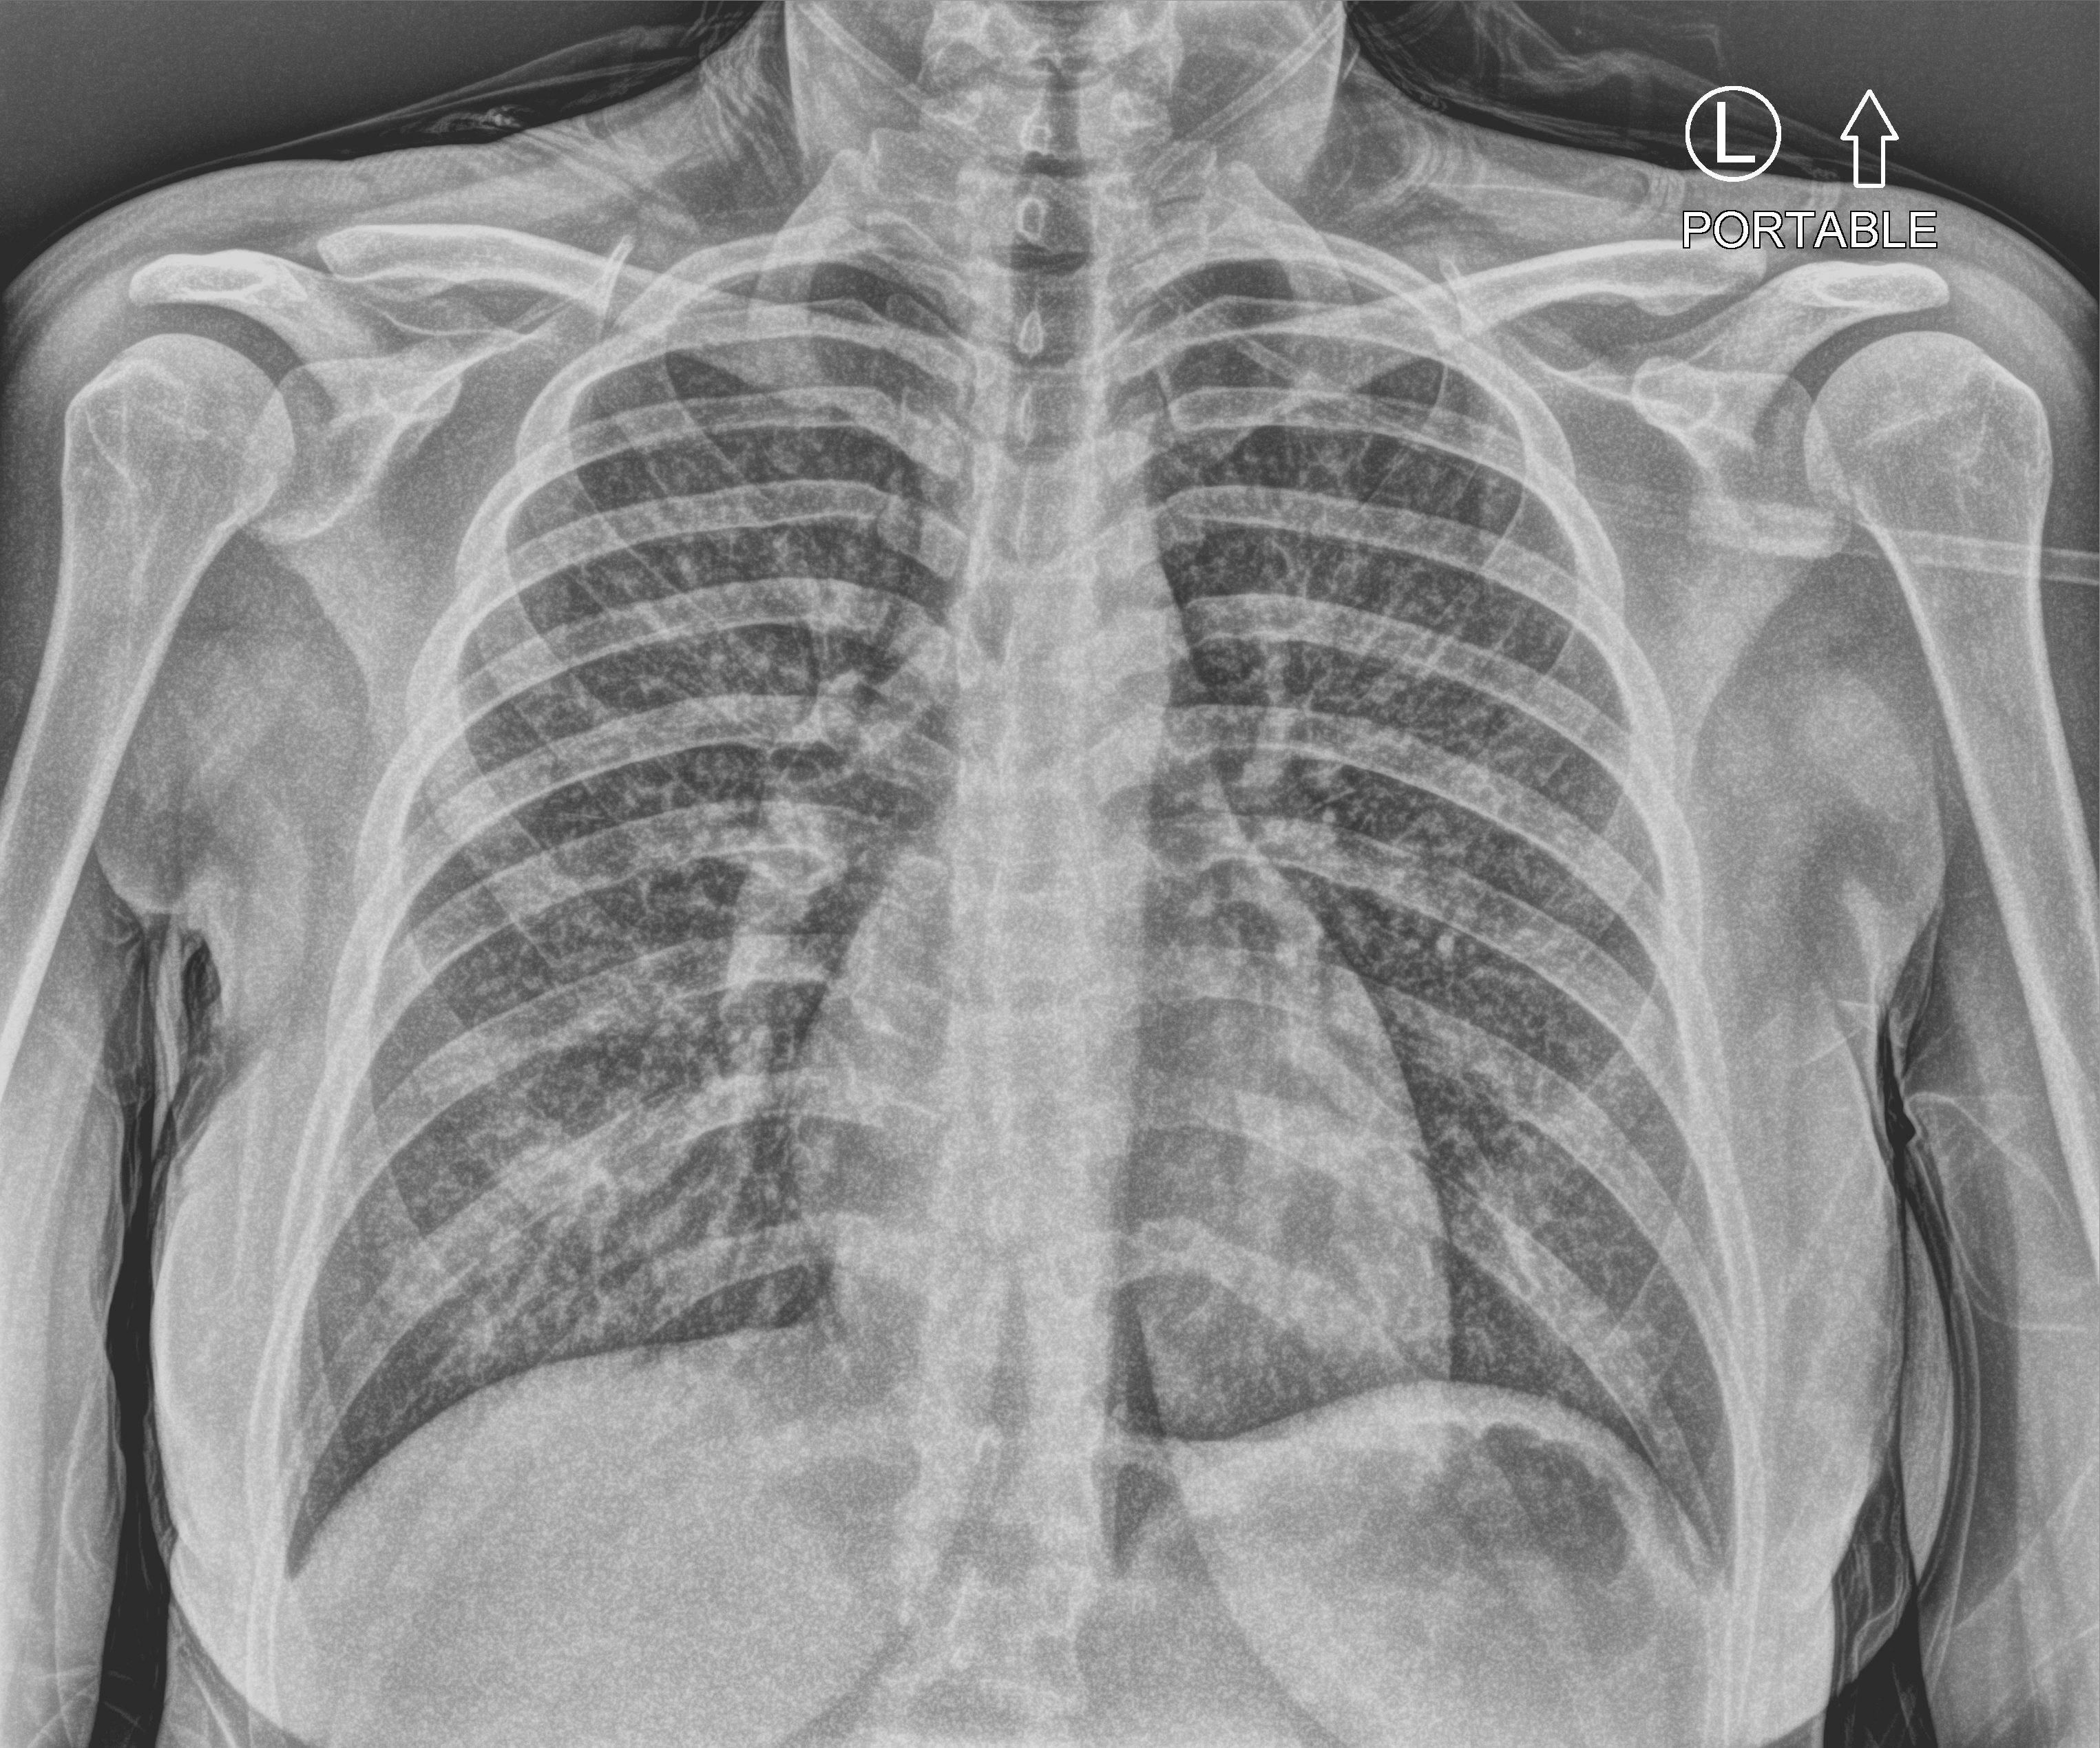
Bedside chest radiograph (computed radiography). Patient hospitalised with COVID-19; female, aged 18–59 years.
Hospital-stay facts (about this admission, not read from this image; timing relative to this image not recorded):
- admitted to intensive care during this hospital stay: no
- mechanically ventilated during this hospital stay: no